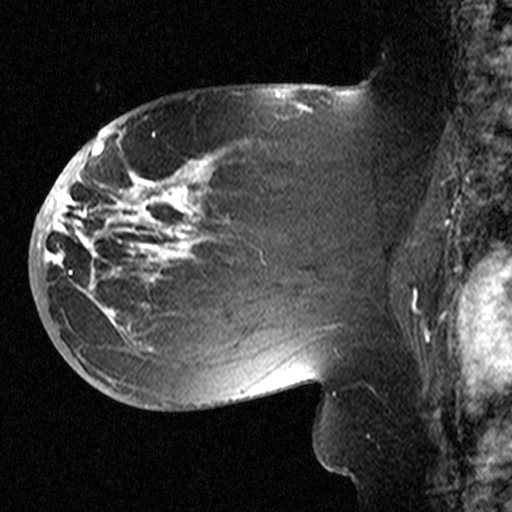
Breast MRI (dynamic contrast-enhanced), one sagittal slice. Slice 25 of 44 in the series (ordered by position). Dynamic contrast-enhanced study with each time point stored as its own series, time point 2 of 3 at this slice position (early post-contrast, ordered by acquisition time). 1.5 T. TE 4.5 ms, TR 11 ms. 512 × 512 image matrix. Patient: female, 53 years. From the clinical record (not read from this slice): setting: breast cancer imaged before/during neoadjuvant chemotherapy; receptor status: HR-positive, HER2-negative.
Annotated regions visible in this slice (semi-automatic segmentation, software-assisted and operator-edited):
- analysis volume of interest (the breast-tissue region the enhancement analysis was run in; not a lesion): bounding box [x1, y1, x2, y2] px = [58, 154, 311, 367]
- tumour enhancement mask (voxels above the 90 % enhancement threshold inside the analysis volume of interest): [58, 159, 208, 336]